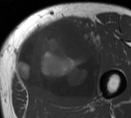
MRI of an extremity soft-tissue mass, one axial slice. Slice 30 of 55 in the series (ordered by position). MR volume resampled by the dataset authors to the PET/CT grid (not the native acquisition matrix). 3.27 mm slice thickness. 131 × 118 image matrix, field of view 128 × 115 mm. Male patient. Case-level facts recorded for this patient, not image findings: histological type: pleiomorphic liposarcoma; grade: high; site of the primary tumour: left thigh.
Annotated regions visible in this slice (expert contour drawn on MRI and transferred to this co-registered scan by the dataset authors):
- gross tumour volume including surrounding oedema: box from (x=14, y=18) to (x=108, y=104) px
- gross tumour volume (mass): (x=14, y=18)–(x=103, y=104)